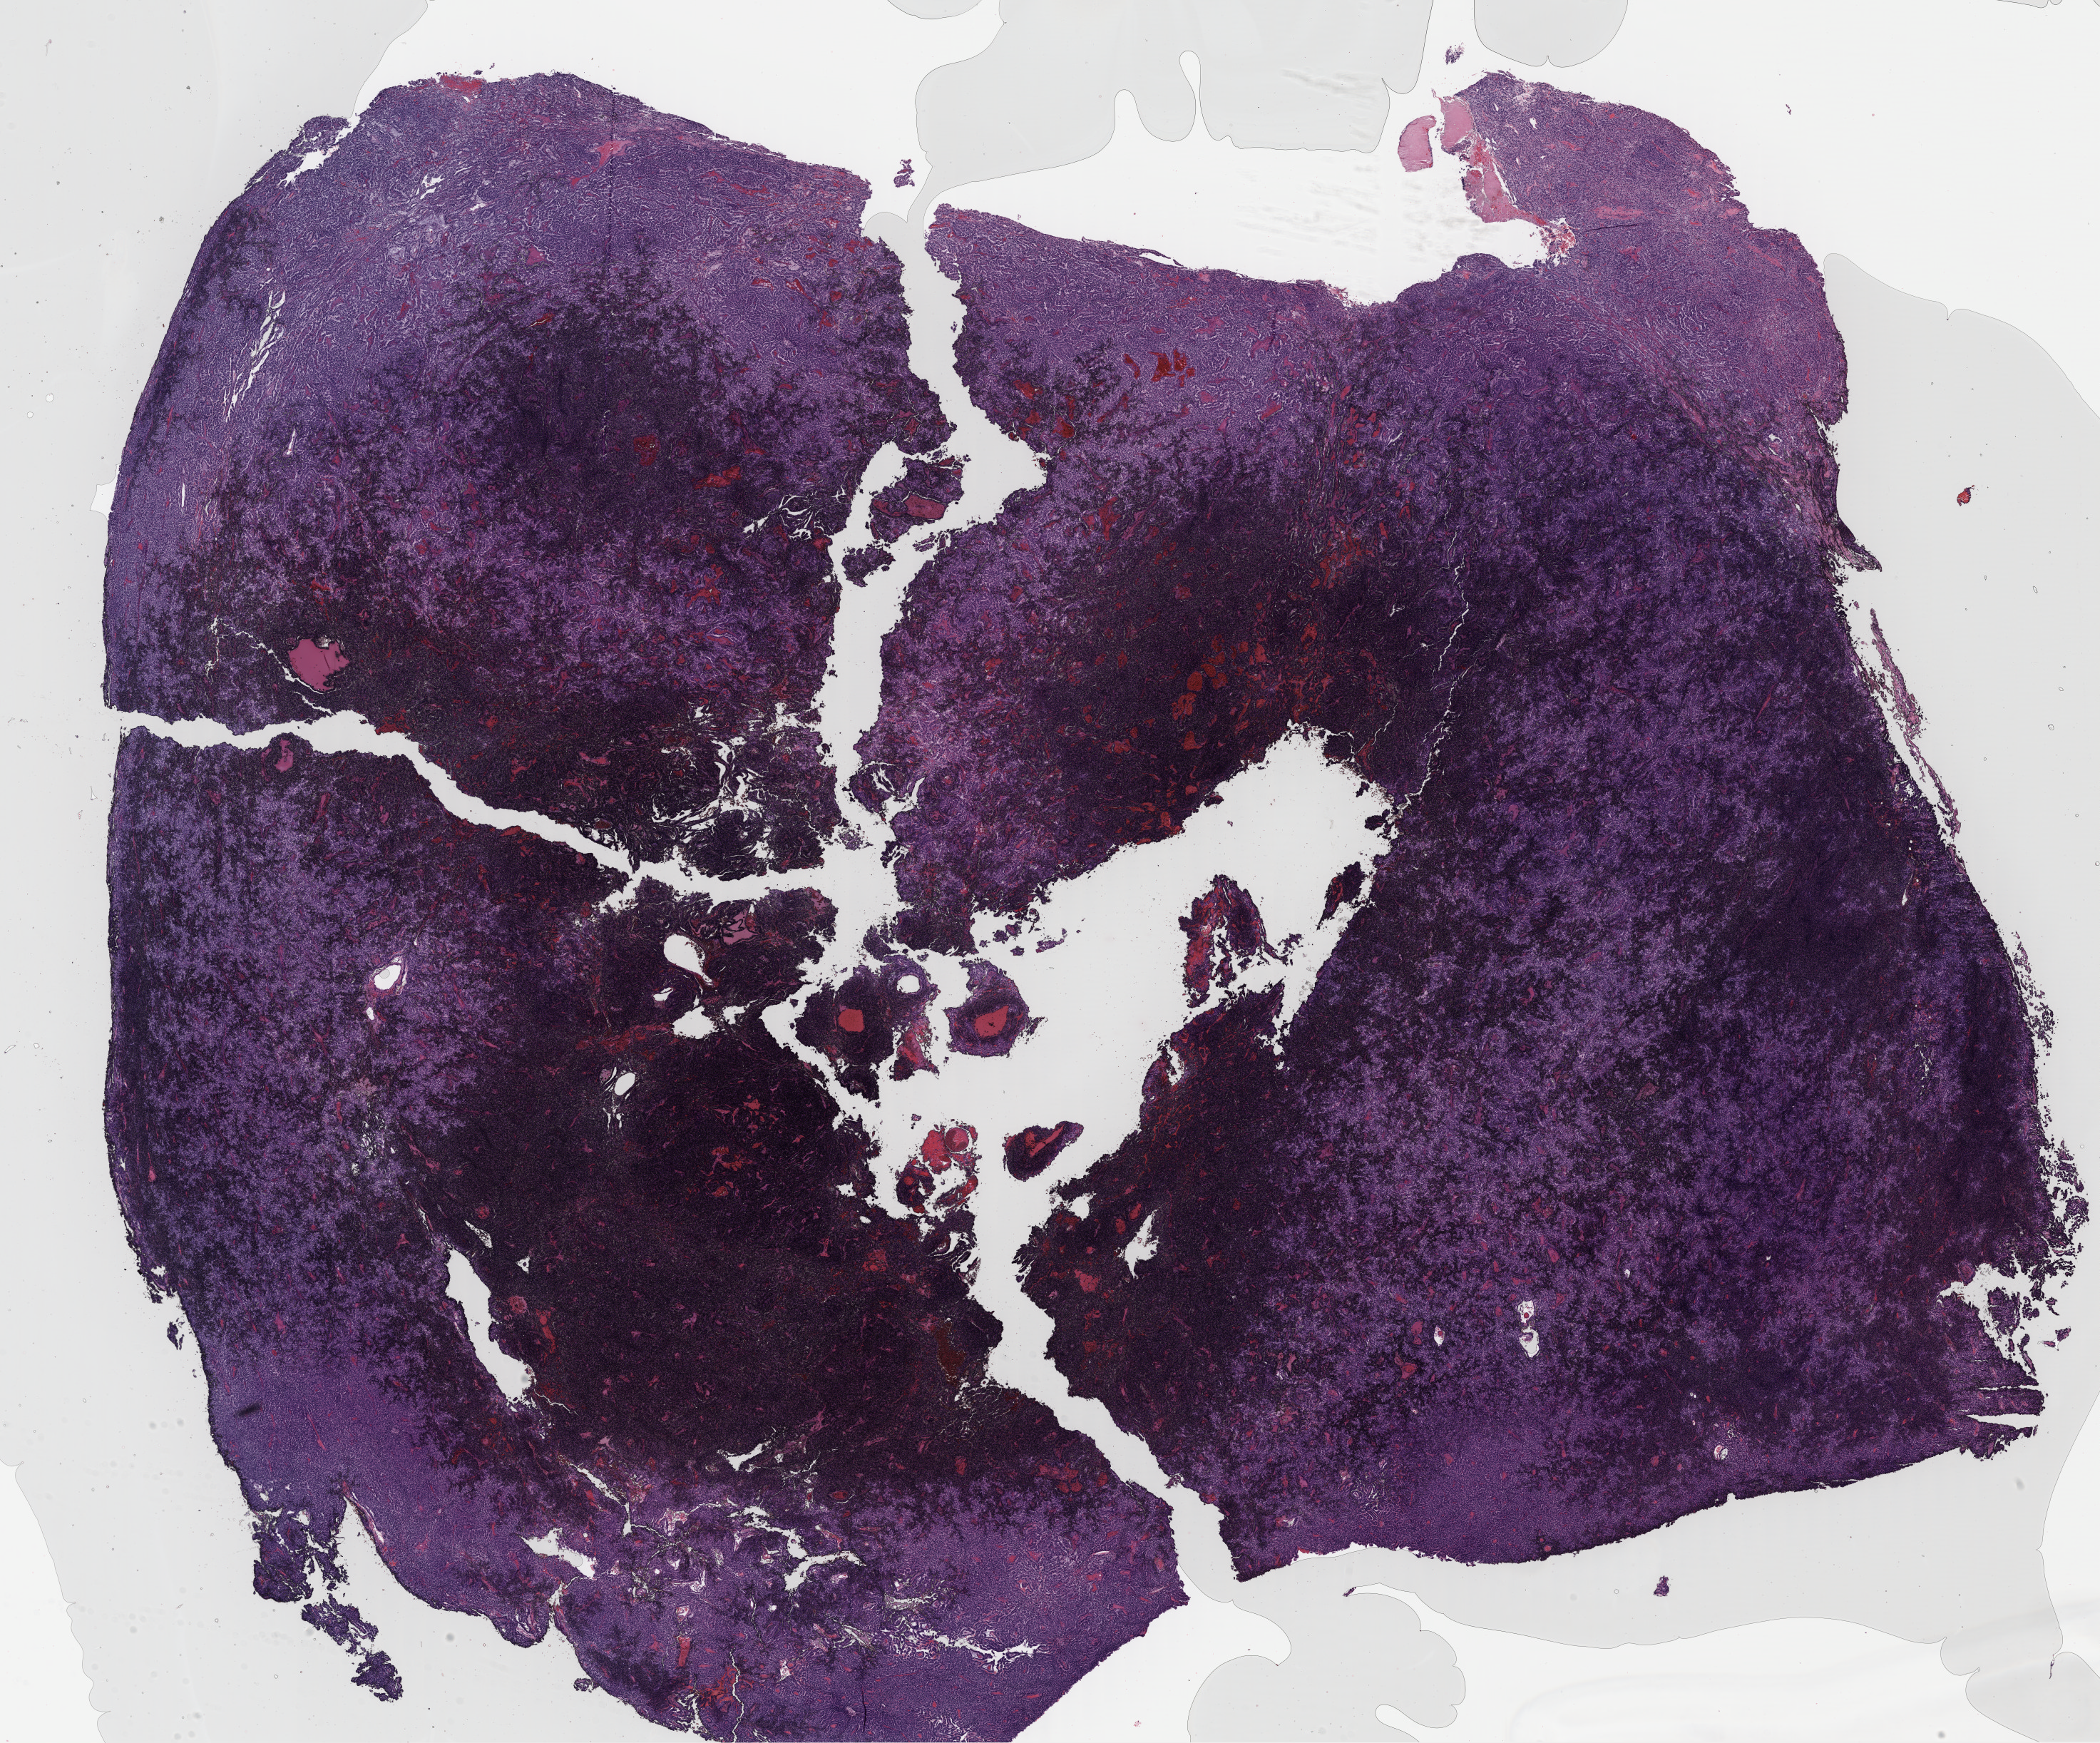
Whole-slide histology image, Hematoxylin and eosin (H&E) stained, whole scanned area (about 23.1 x 19.2 mm) shown as a low-resolution overview. Formalin-fixed paraffin-embedded (FFPE) diagnostic section. Kidney, primary tumour sample. Patient: male, age at initial diagnosis 79 years.
- pathologic diagnosis: Papillary adenocarcinoma, NOS
- AJCC pathologic stage: III (7th edition)